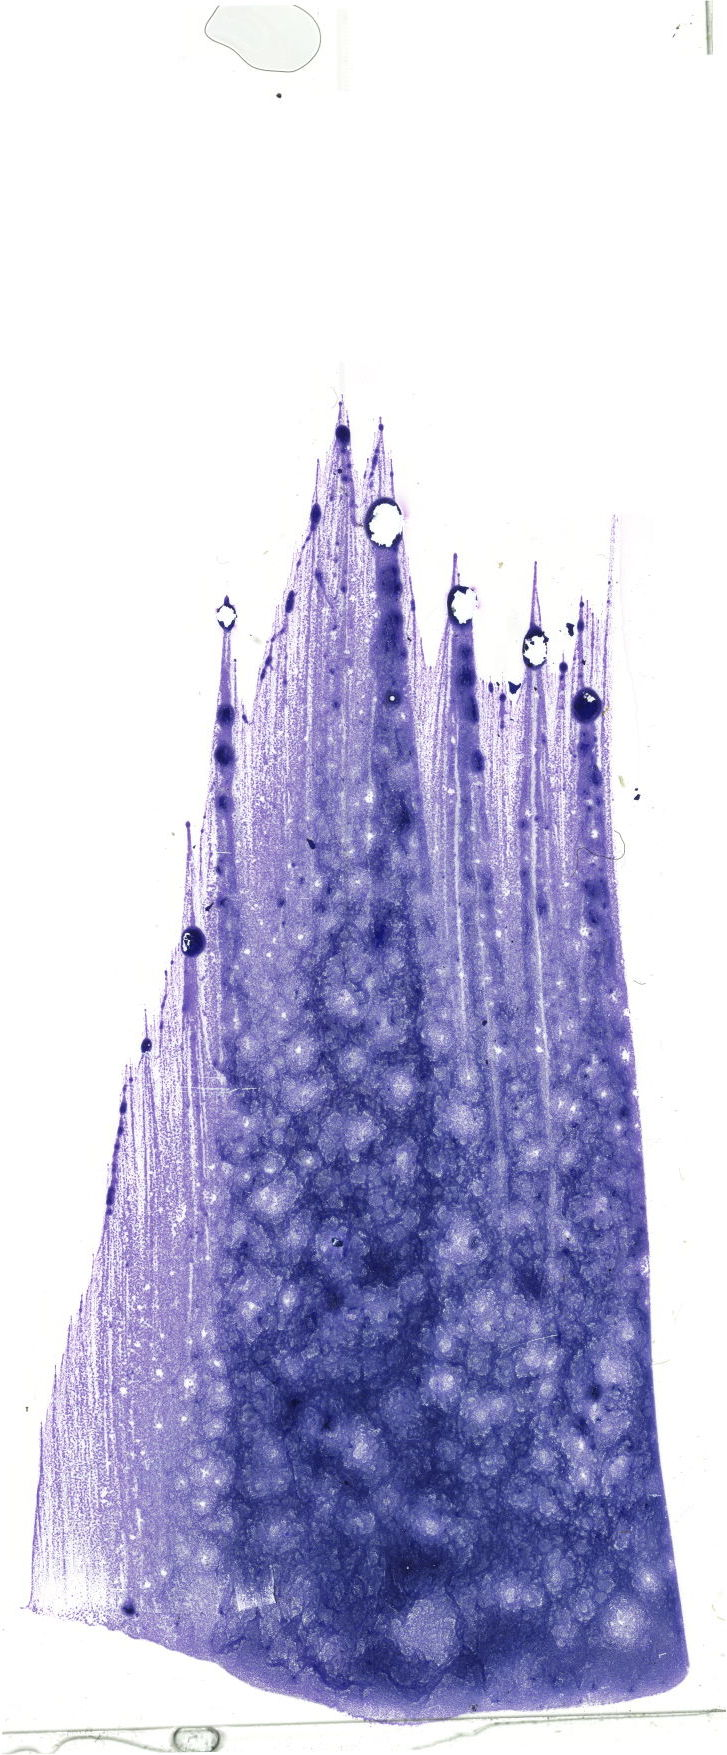
May-Grünwald–Giemsa-stained marrow aspirate smear (whole slide), whole scanned area (about 20.6 x 49.7 mm) shown as a low-resolution overview. Patient sex: female.
Diagnosis: Chronic Phase Chronic Myeloid Leukemia, BCR-ABL1 Positive.